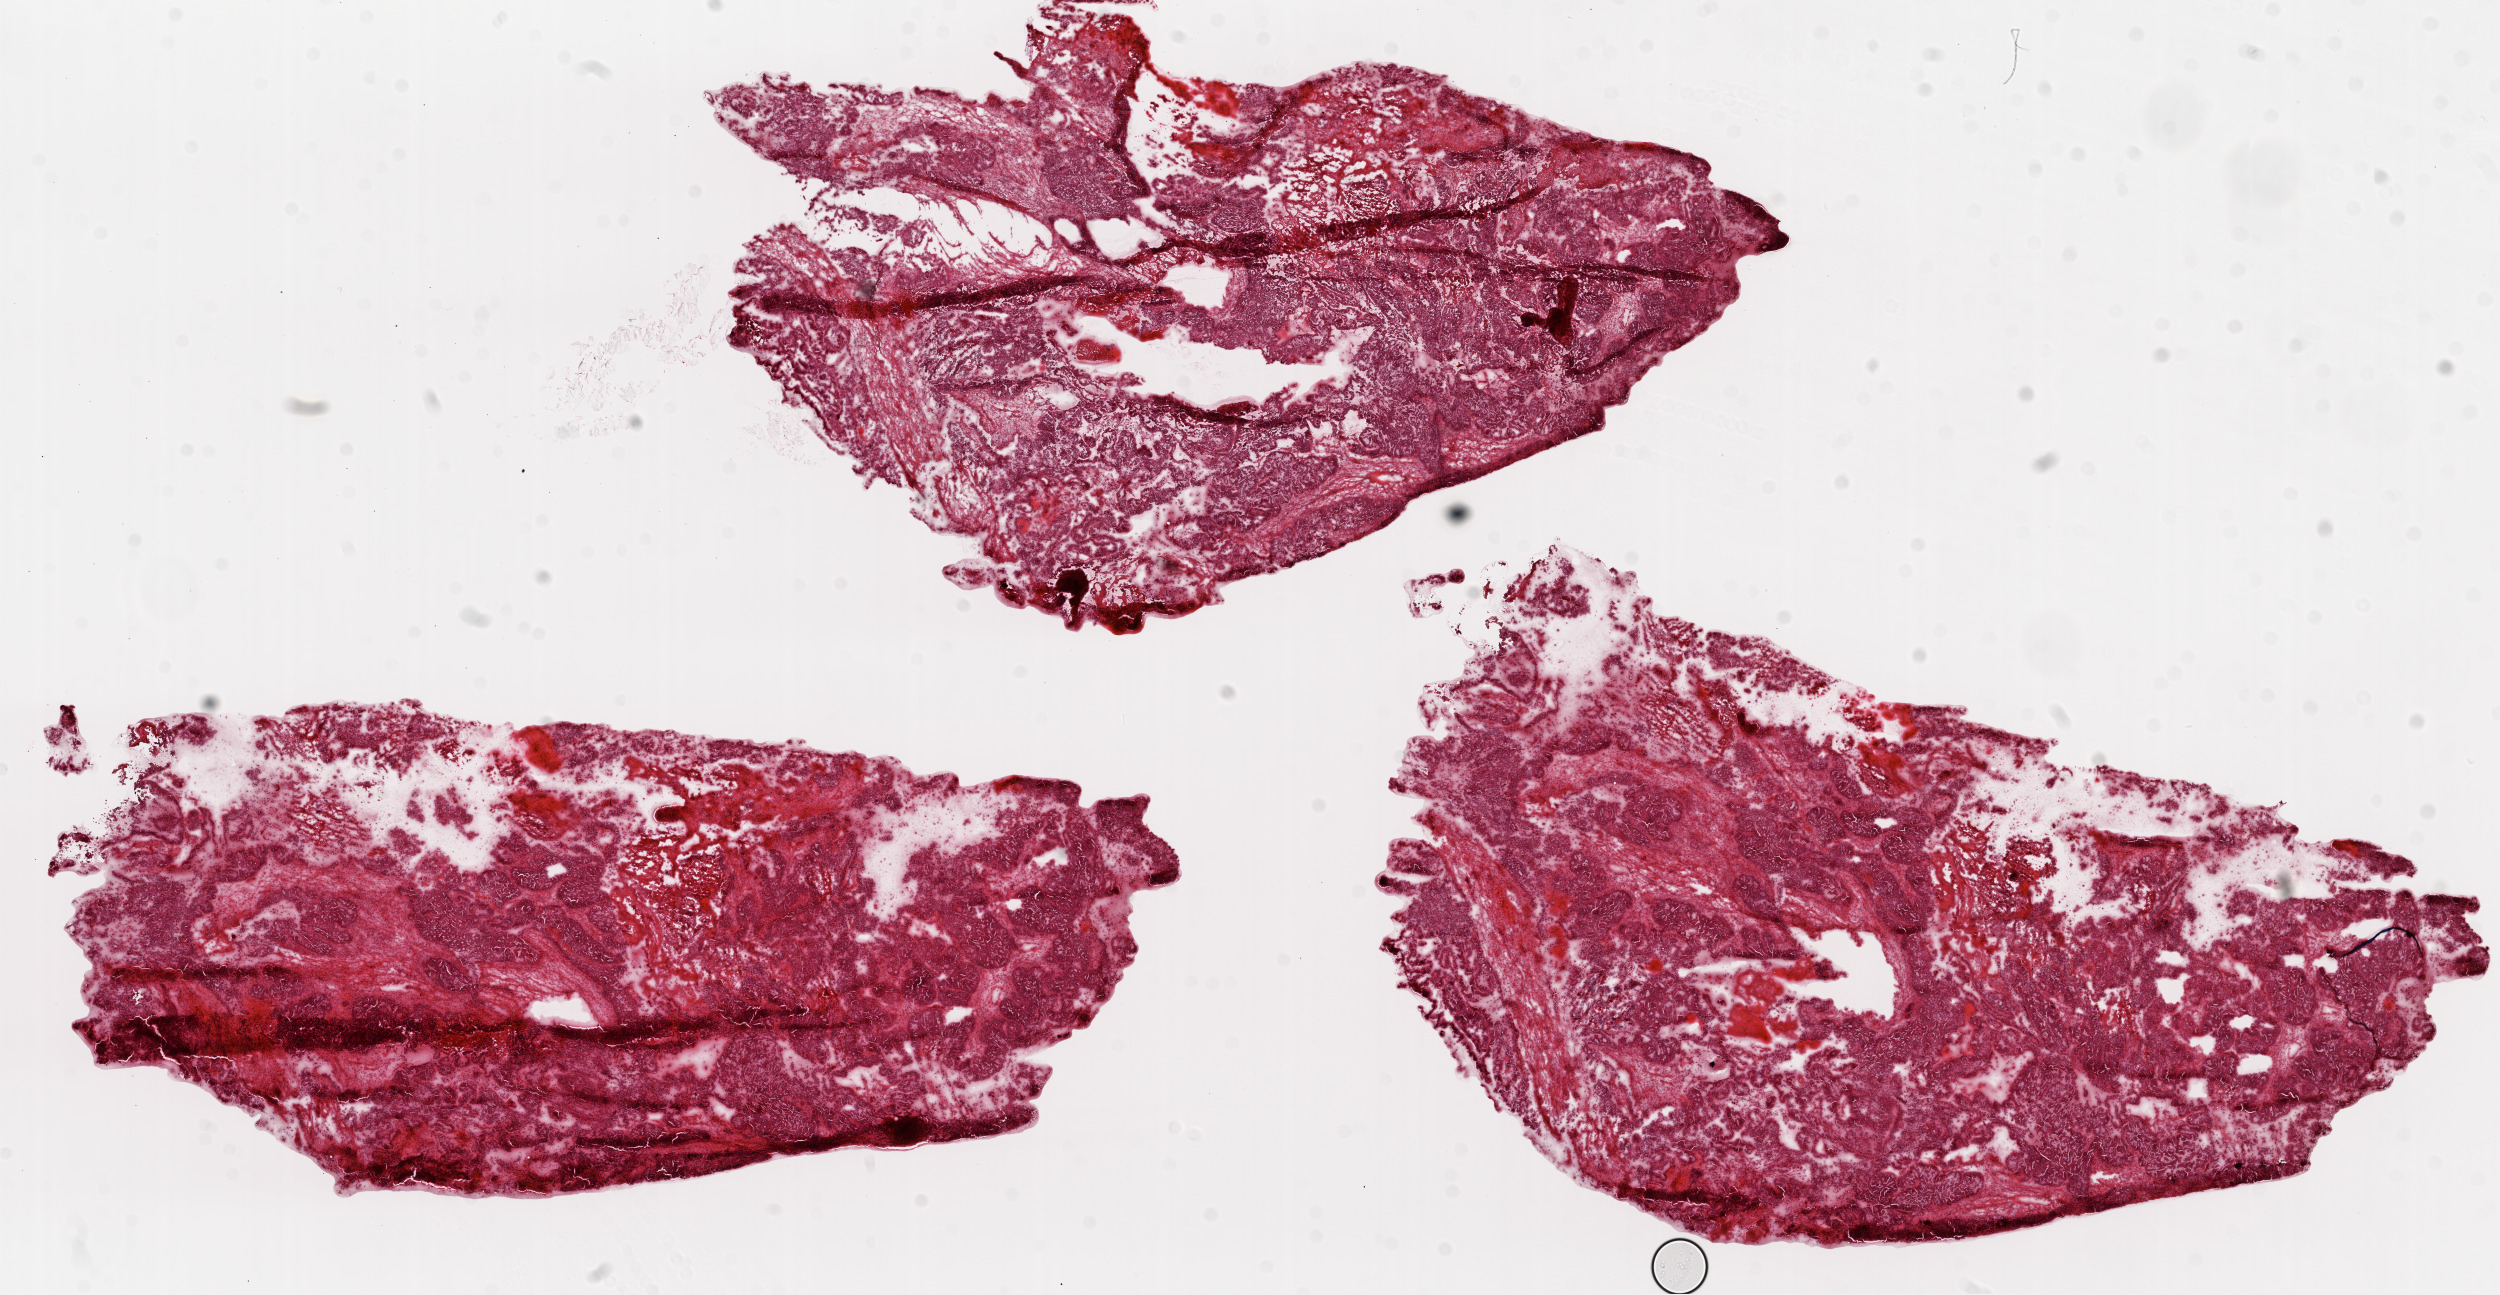
Digitized Hematoxylin and eosin (H&E) stained tissue section (whole slide), low-resolution overview of the scanned area, about 20.1 x 10.4 mm (acquisition: 20x scan). Frozen section. Primary tumour sample from the ovary. Female patient; age at initial diagnosis 51 years. Pathologist review of this section (percent, as recorded): tumour cells 50%, tumour nuclei 85%.
Diagnosis: Serous cystadenocarcinoma, NOS.